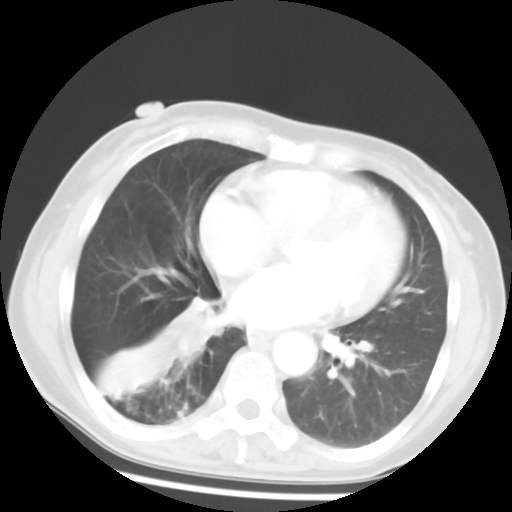
Chest CT, one axial slice; position 23 of 52 along the scan axis; reconstruction kernel STANDARD; 120 kVp; lung window (W 1500 / L -600 HU); 5 mm slice thickness; 512 × 512 image matrix, field of view 297 × 297 mm. Patient: female, 54 years. Case-level facts recorded for this patient, not image findings: clinical TNM (as recorded): T1c N0 M0; histopathological grade: G1-2.
Structures marked on this image (rectangle marked by the reading radiologist):
- lung tumour (recorded histology: squamous cell carcinoma): bounding box (x1, y1, x2, y2) in pixels: (169, 286, 228, 363)